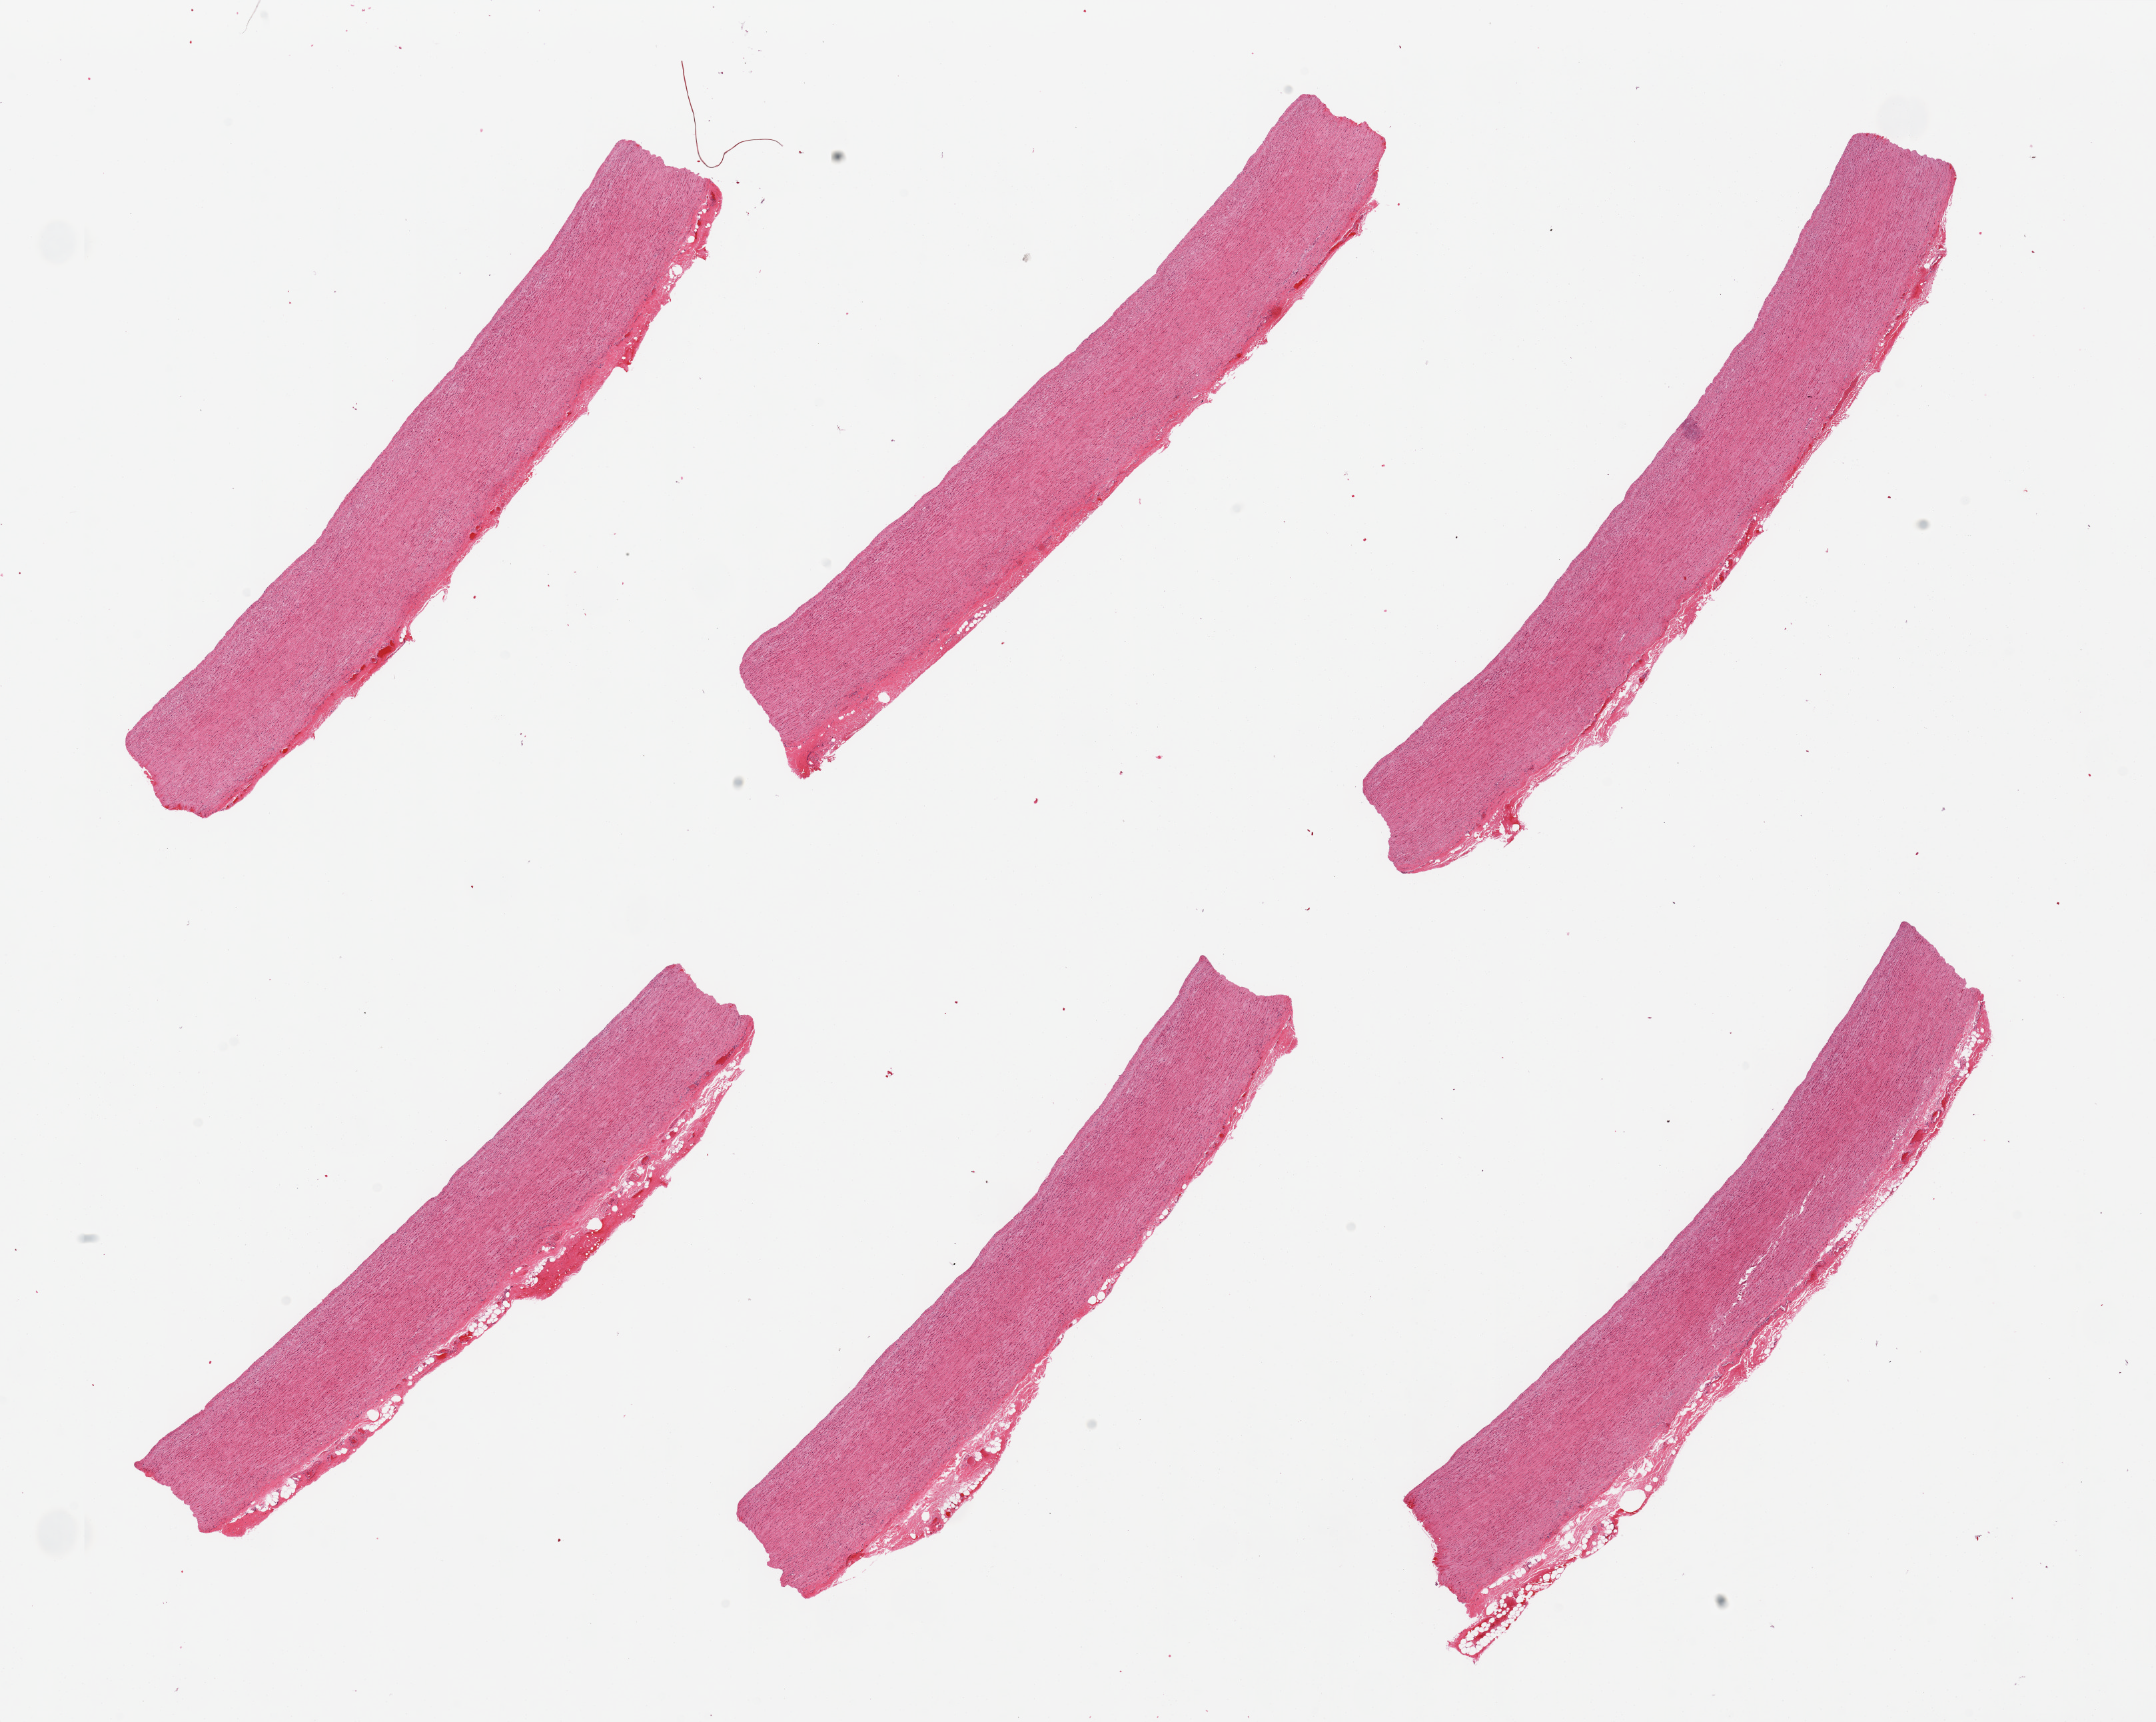
Whole-slide image, hematoxylin and eosin (H&E) stain, brightfield, a low-resolution overview of the entire scanned area, about 25.6 x 20.4 mm (acquisition: 20x scan), PAXgene-fixed paraffin-embedded (PFPE) section, sampled site (target tissue): aorta, tissue donor sample.
• review note (as recorded): 6 pieces, minimal visible atherosis